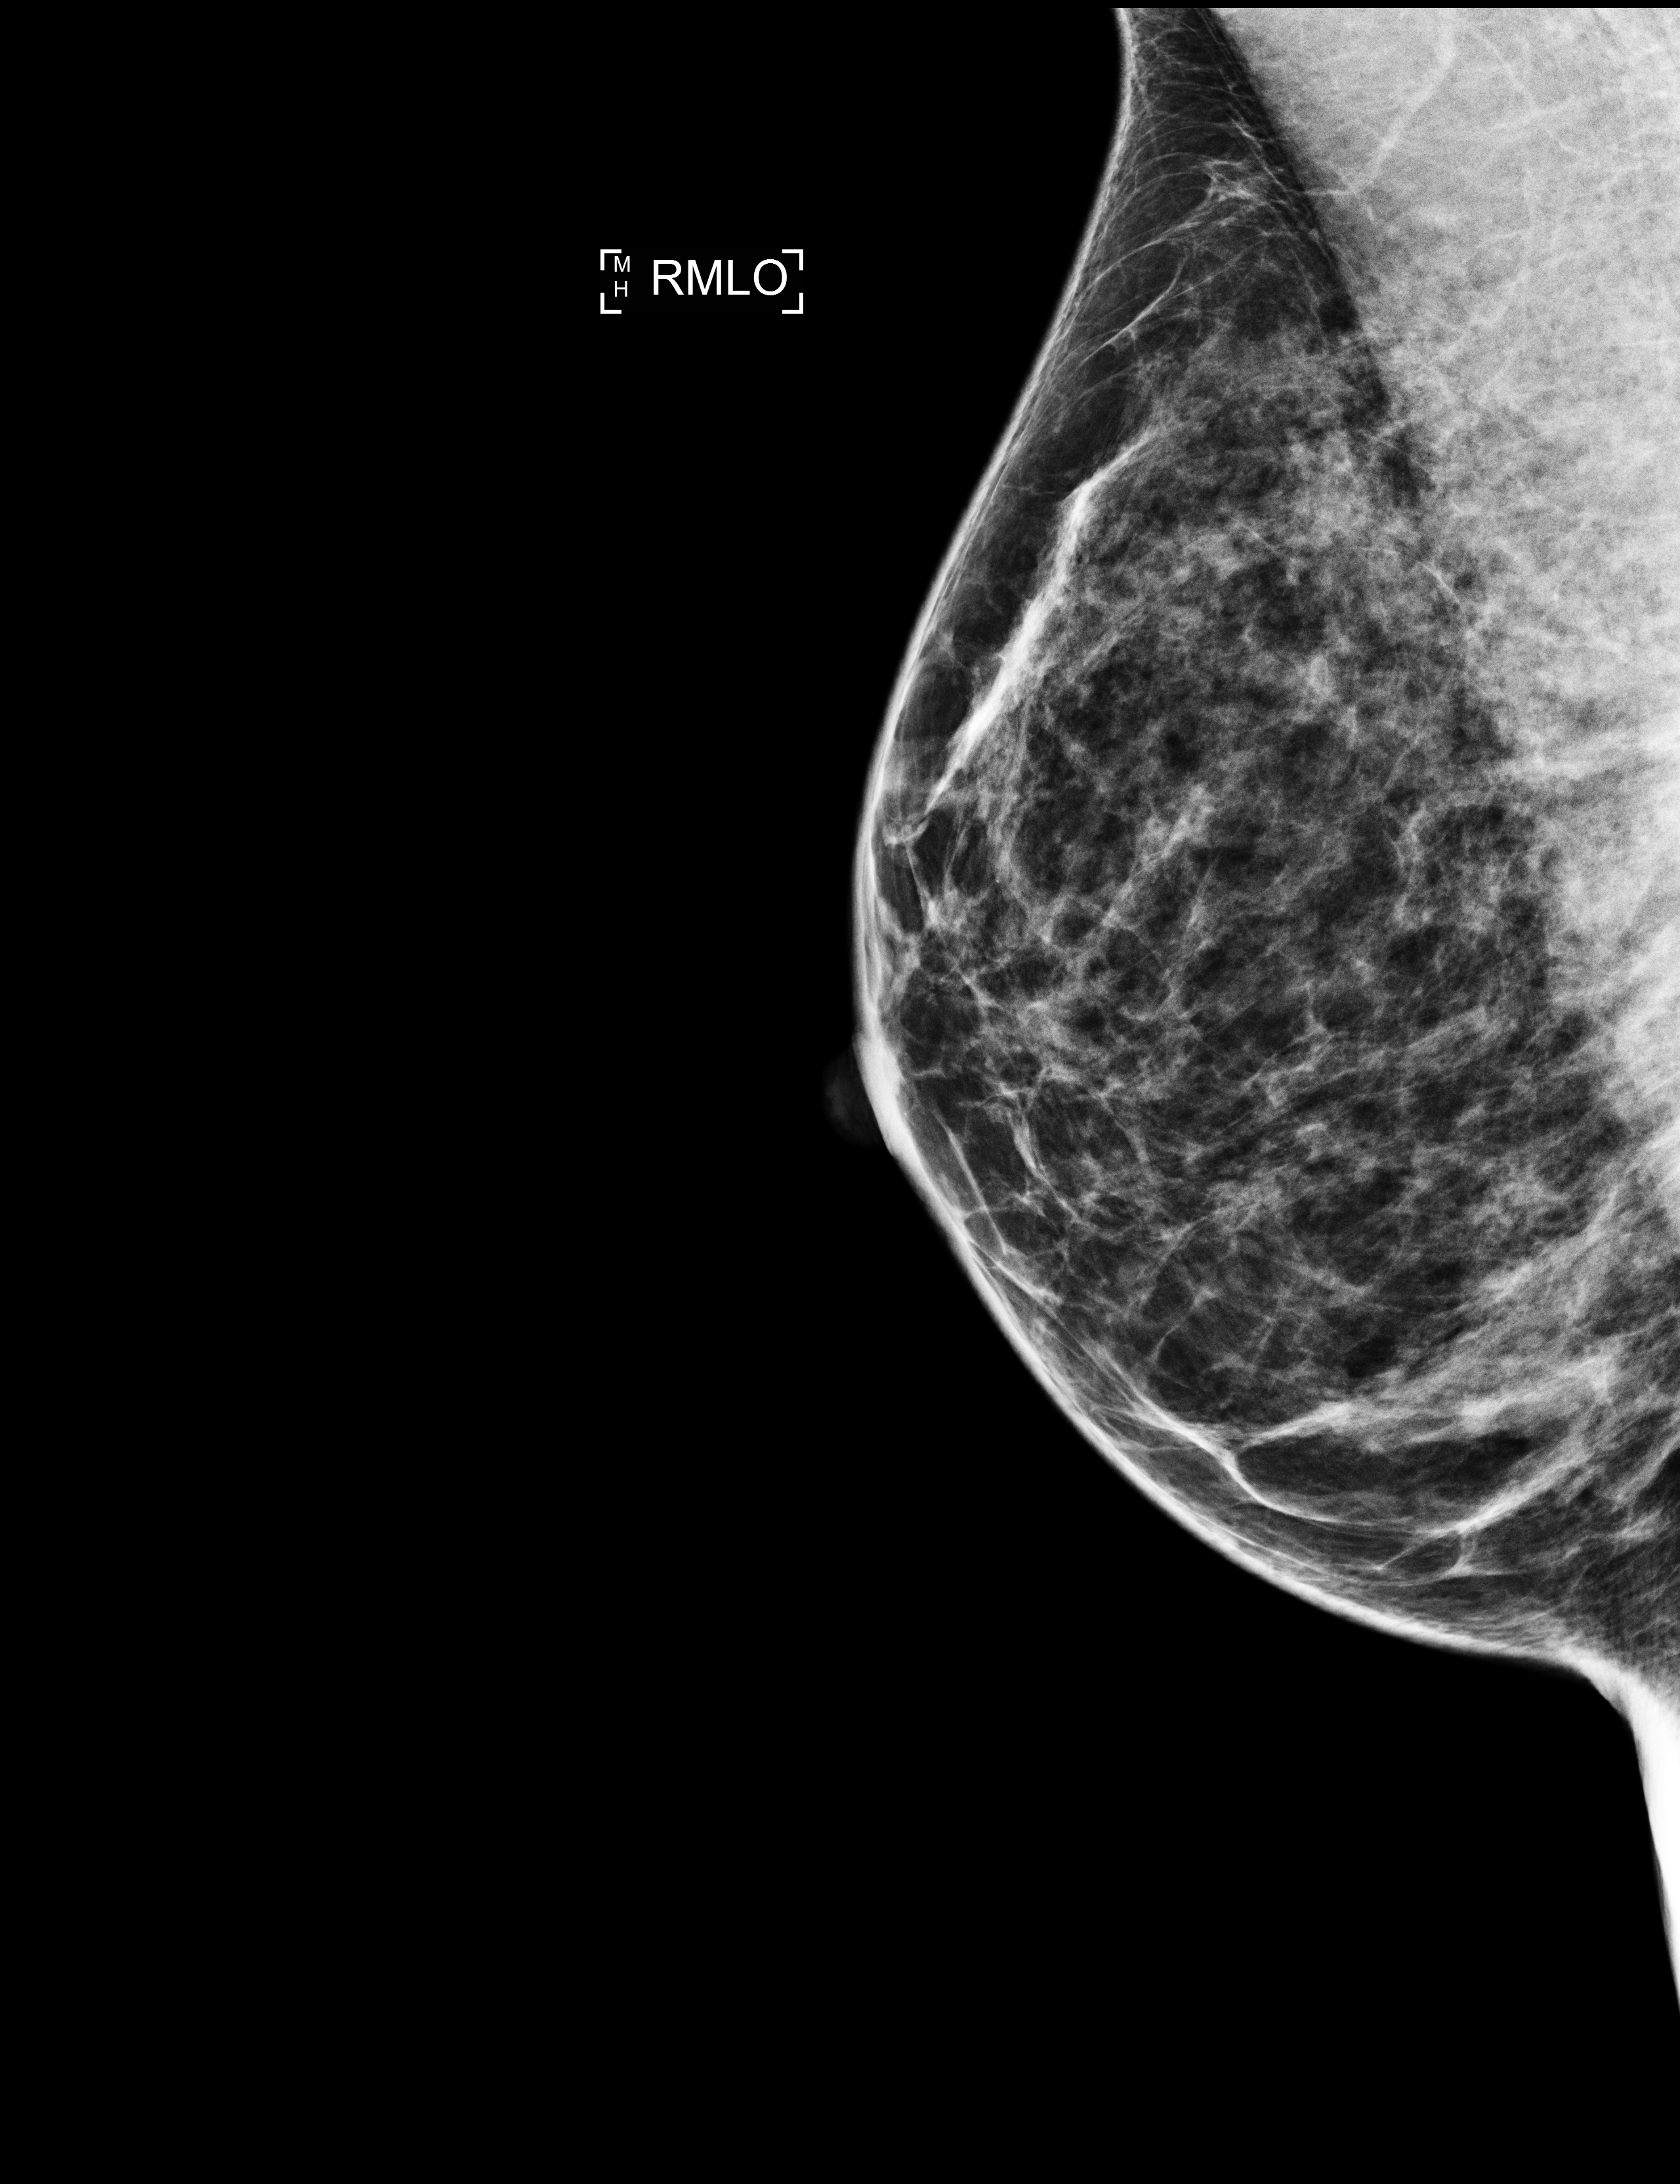
Screening examination, compressed breast thickness 50 mm. Patient aged 42 years (female).
Image type: full-field digital mammogram. Breast: right. Projection: mediolateral oblique (MLO) view.